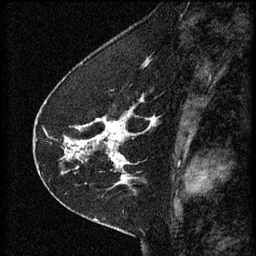
Breast MRI (dynamic contrast-enhanced), one sagittal slice. Slice 24 of 60 in the series (ordered by position). 3 images stored at this slice position (order not interpretable as contrast timing). 1.5 T. TE 4.2 ms, TR 8.2 ms. 2 mm slice thickness. 256 × 256 image matrix, field of view 180 × 180 mm. Patient: female, 41 years.
Outlined on this slice (semi-automatic segmentation, software-assisted and operator-edited):
- analysis volume of interest (the breast-tissue region the enhancement analysis was run in; not a lesion): bounding box [x1, y1, x2, y2] px = [67, 96, 154, 173]
- tumour enhancement mask (voxels above the 70 % enhancement threshold inside the analysis volume of interest): [67, 112, 154, 169]